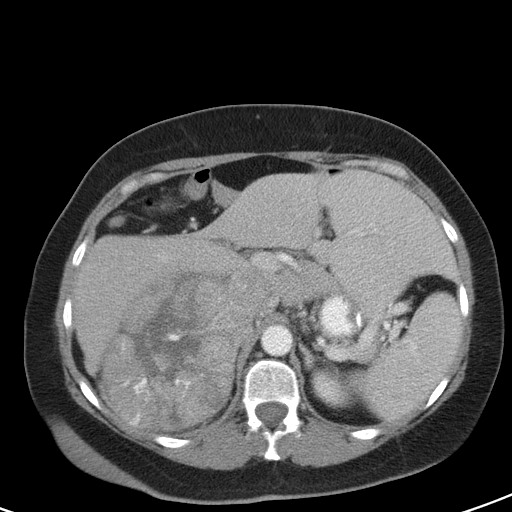
Contrast-enhanced abdominal CT, one axial slice; slice 74 of 126 in the series (ordered by position); 120 kVp; intravenous contrast given; soft-tissue window (W 400 / L 40 HU); 5 mm slice thickness; 512 × 512 image matrix, field of view 356 × 356 mm. Female patient, age 51 years. From the clinical record (not read from this slice): diagnosis: adrenocortical carcinoma; tumour side: right adrenal; tumour size at pathology: 17 cm; Ki-67 index: 12 %; stage (as recorded): 2.
Structures marked on this image (semi-automatic segmentation, software-assisted and operator-edited):
- mass: bounding box [x1, y1, x2, y2] px = [103, 270, 266, 430]